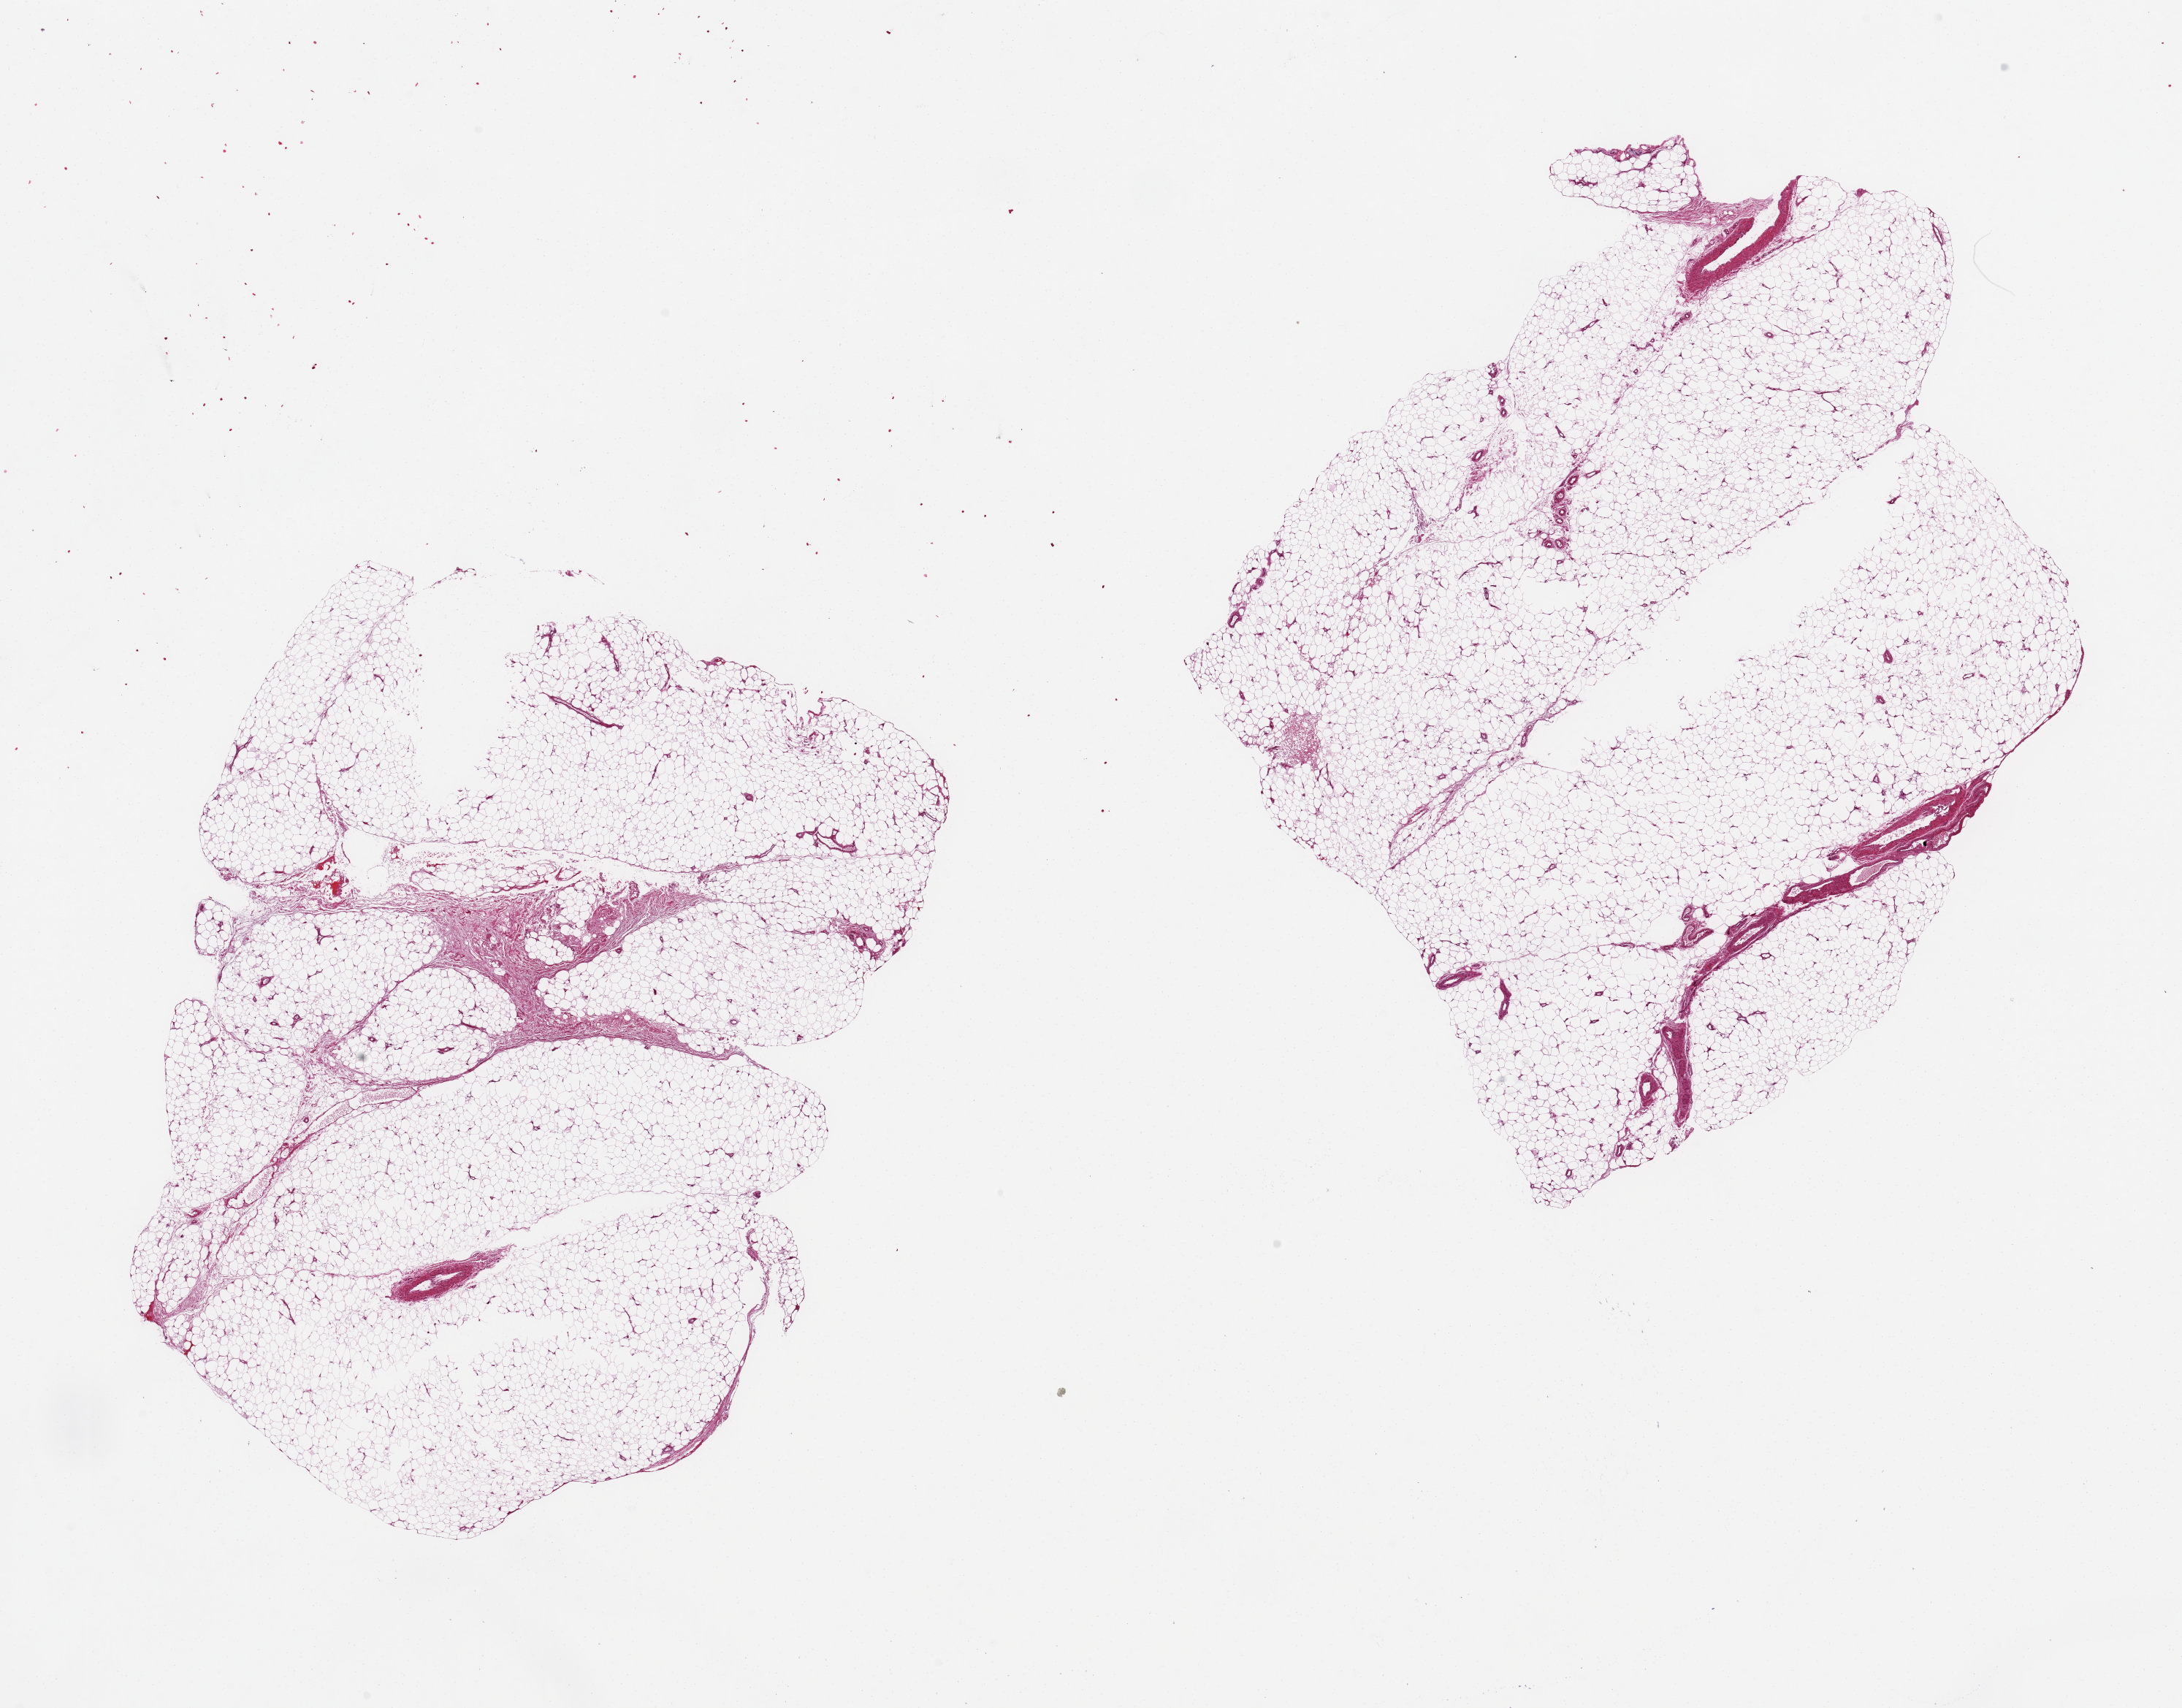
Whole-slide image, haematoxylin and eosin stain — shown as a low-resolution overview of the whole scanned area (about 23.6 x 18.5 mm, acquisition: 20x scan), PAXgene-fixed paraffin-embedded (PFPE) section, target tissue: adipose tissue, tissue donor sample. Male donor.
Review note (as recorded): 2 pieces 10x7 & 8x6 mm; good specimen.